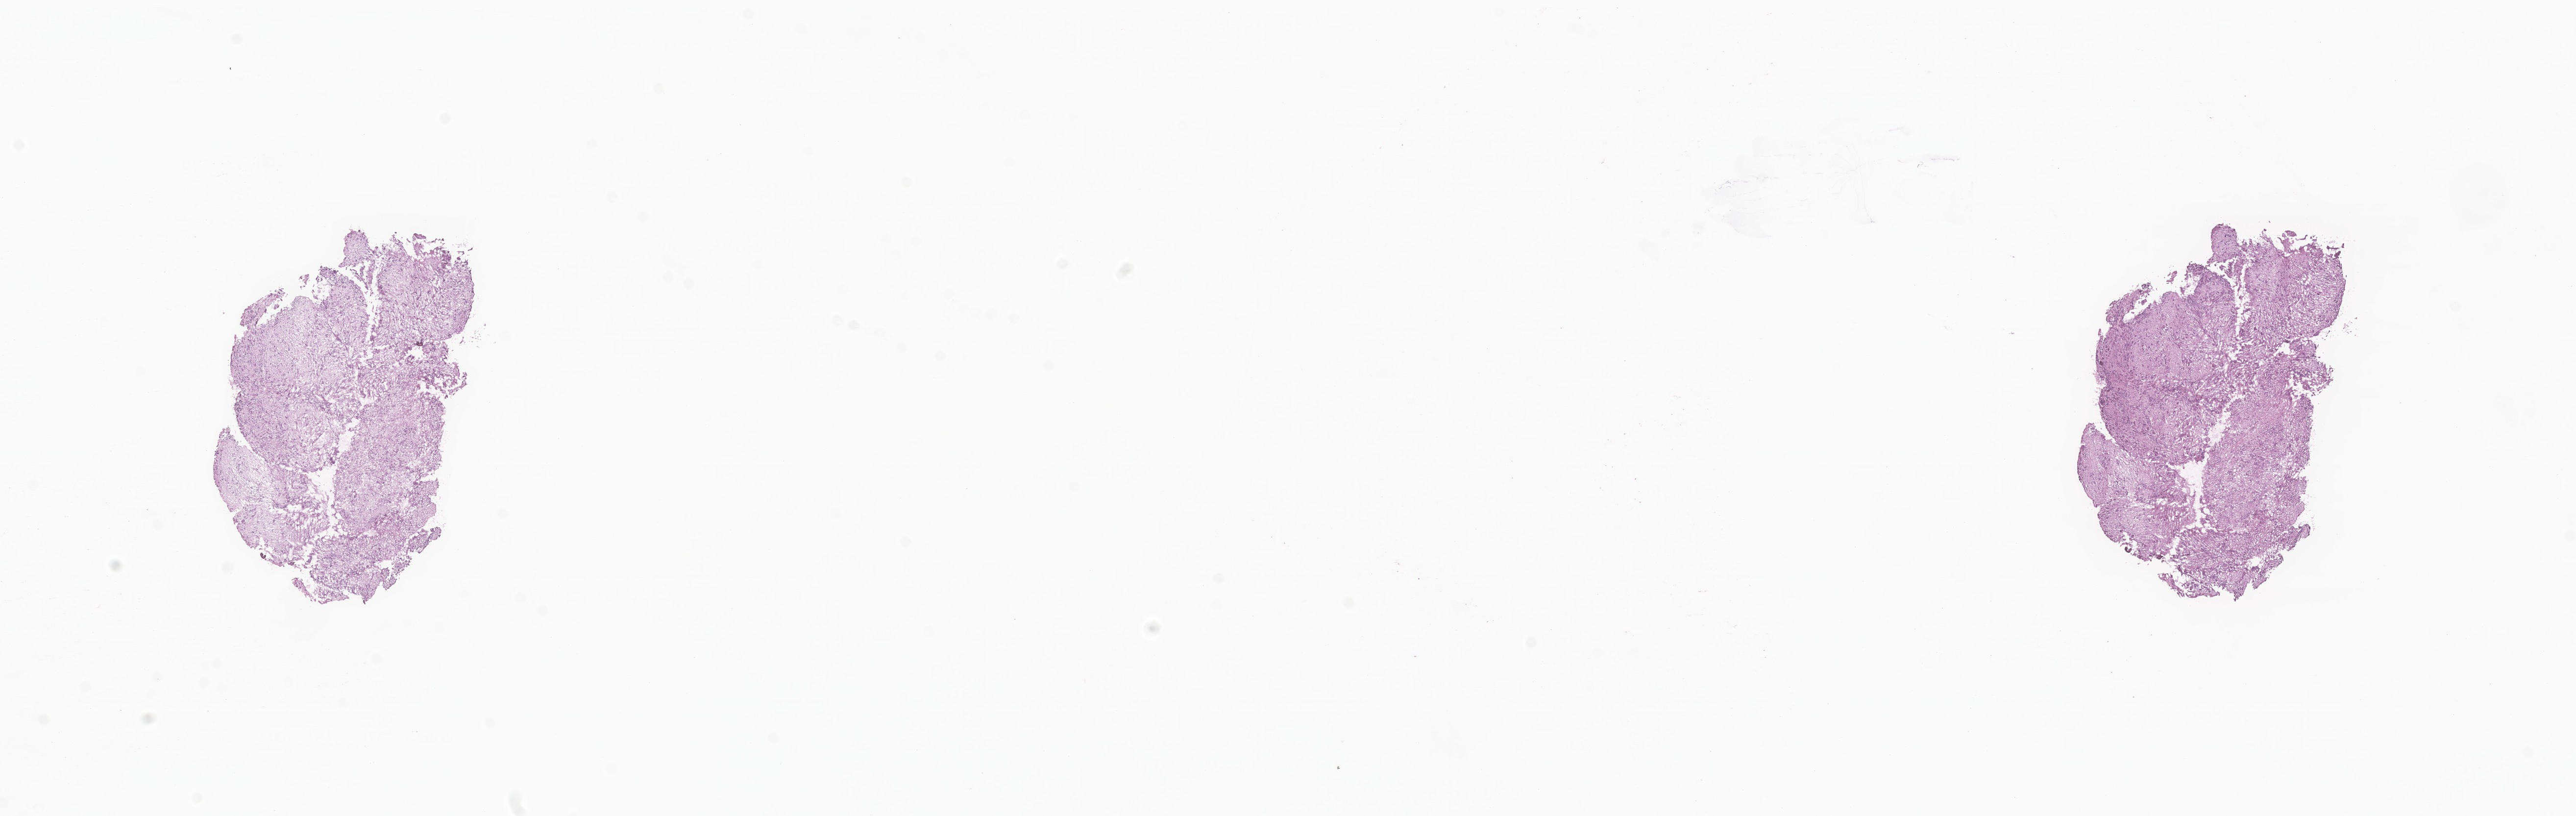
Digitized hematoxylin and eosin (H&E)-stained section of tumor tissue from the spinal cord, a low-resolution overview of the entire scanned area, about 22.2 x 7.0 mm, frozen section (OCT-embedded). Patient: male, age 70 months (5 years 10 months).
• diagnosis: Ganglioglioma, NOS